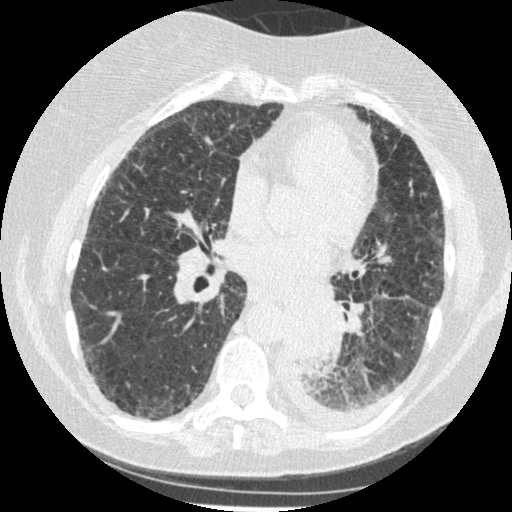
Low-dose screening chest CT, one axial slice; position 109 of 341 along the scan axis; reconstruction kernel STANDARD; lung window (W 1500 / L -600 HU); 512 × 512 image matrix.
Outlined on this slice (outlined manually by an expert reader):
- lesion 1 (tumor, lower lobe of left lung): bounding box <285,302,338,365> (left, top, right, bottom; pixels)